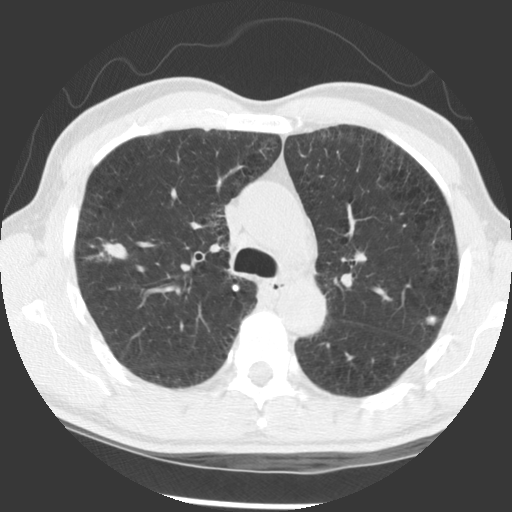
Axial slice from a low-dose chest CT screening exam, first (baseline) screen, lung window (W 1500 / L -600 HU), 2.5 mm slice thickness, 140 kVp, 512 × 512 image matrix. Male participant, aged 56 years at enrolment. Current smoker at enrolment.
- Expert-annotated lung lesion, box from (x=65, y=225) to (x=133, y=278) px.
- Reader record for this screening exam (exam-level; its link to the box is not recorded): non-calcified nodule or mass ≥4 mm, right upper lobe, 12 × 7 mm, spiculated (stellate) margins, soft tissue attenuation.
- Official screen result: positive, change unspecified: nodule(s) >= 4 mm or enlarging nodule(s), mass(es), or other non-specific abnormalities suspicious for lung cancer.